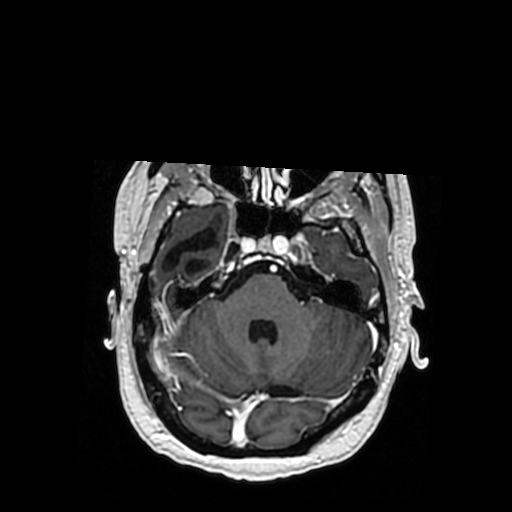
Brain MRI from a brain-tumour surgery series, one axial slice. Position 250 of 364 along the scan axis. T1-weighted post-contrast. 0.5 mm slice thickness. 512 × 512 image matrix, field of view 260 × 260 mm. Case-level facts recorded for this patient, not image findings: histopathology: Oligodendroglioma; WHO grade: 3; IDH mutation: yes; tumour location: Right Posterior Temporal Inferior Parietal.
Annotated regions visible in this slice (manually delineated by an expert):
- previous resection cavity: bounding box (x1, y1, x2, y2) in pixels: (163, 226, 218, 274)